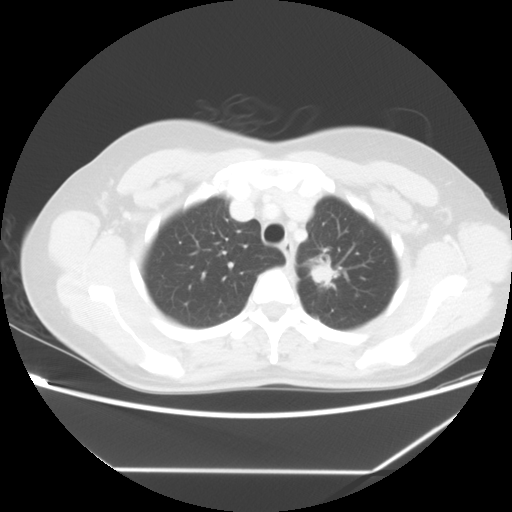
Chest CT, one axial slice. Reconstruction kernel STANDARD. Lung window (W 1500 / L -600 HU). 512 × 512 image matrix, field of view 367 × 367 mm. Patient: female, 43 years. Case-level facts recorded for this patient, not image findings: clinical TNM (as recorded): T1c N0 M1b.
Structures marked on this image (bounding box drawn by a radiologist):
- lung tumour (recorded histology: adenocarcinoma): bounding box <309,260,339,292> (left, top, right, bottom; pixels)